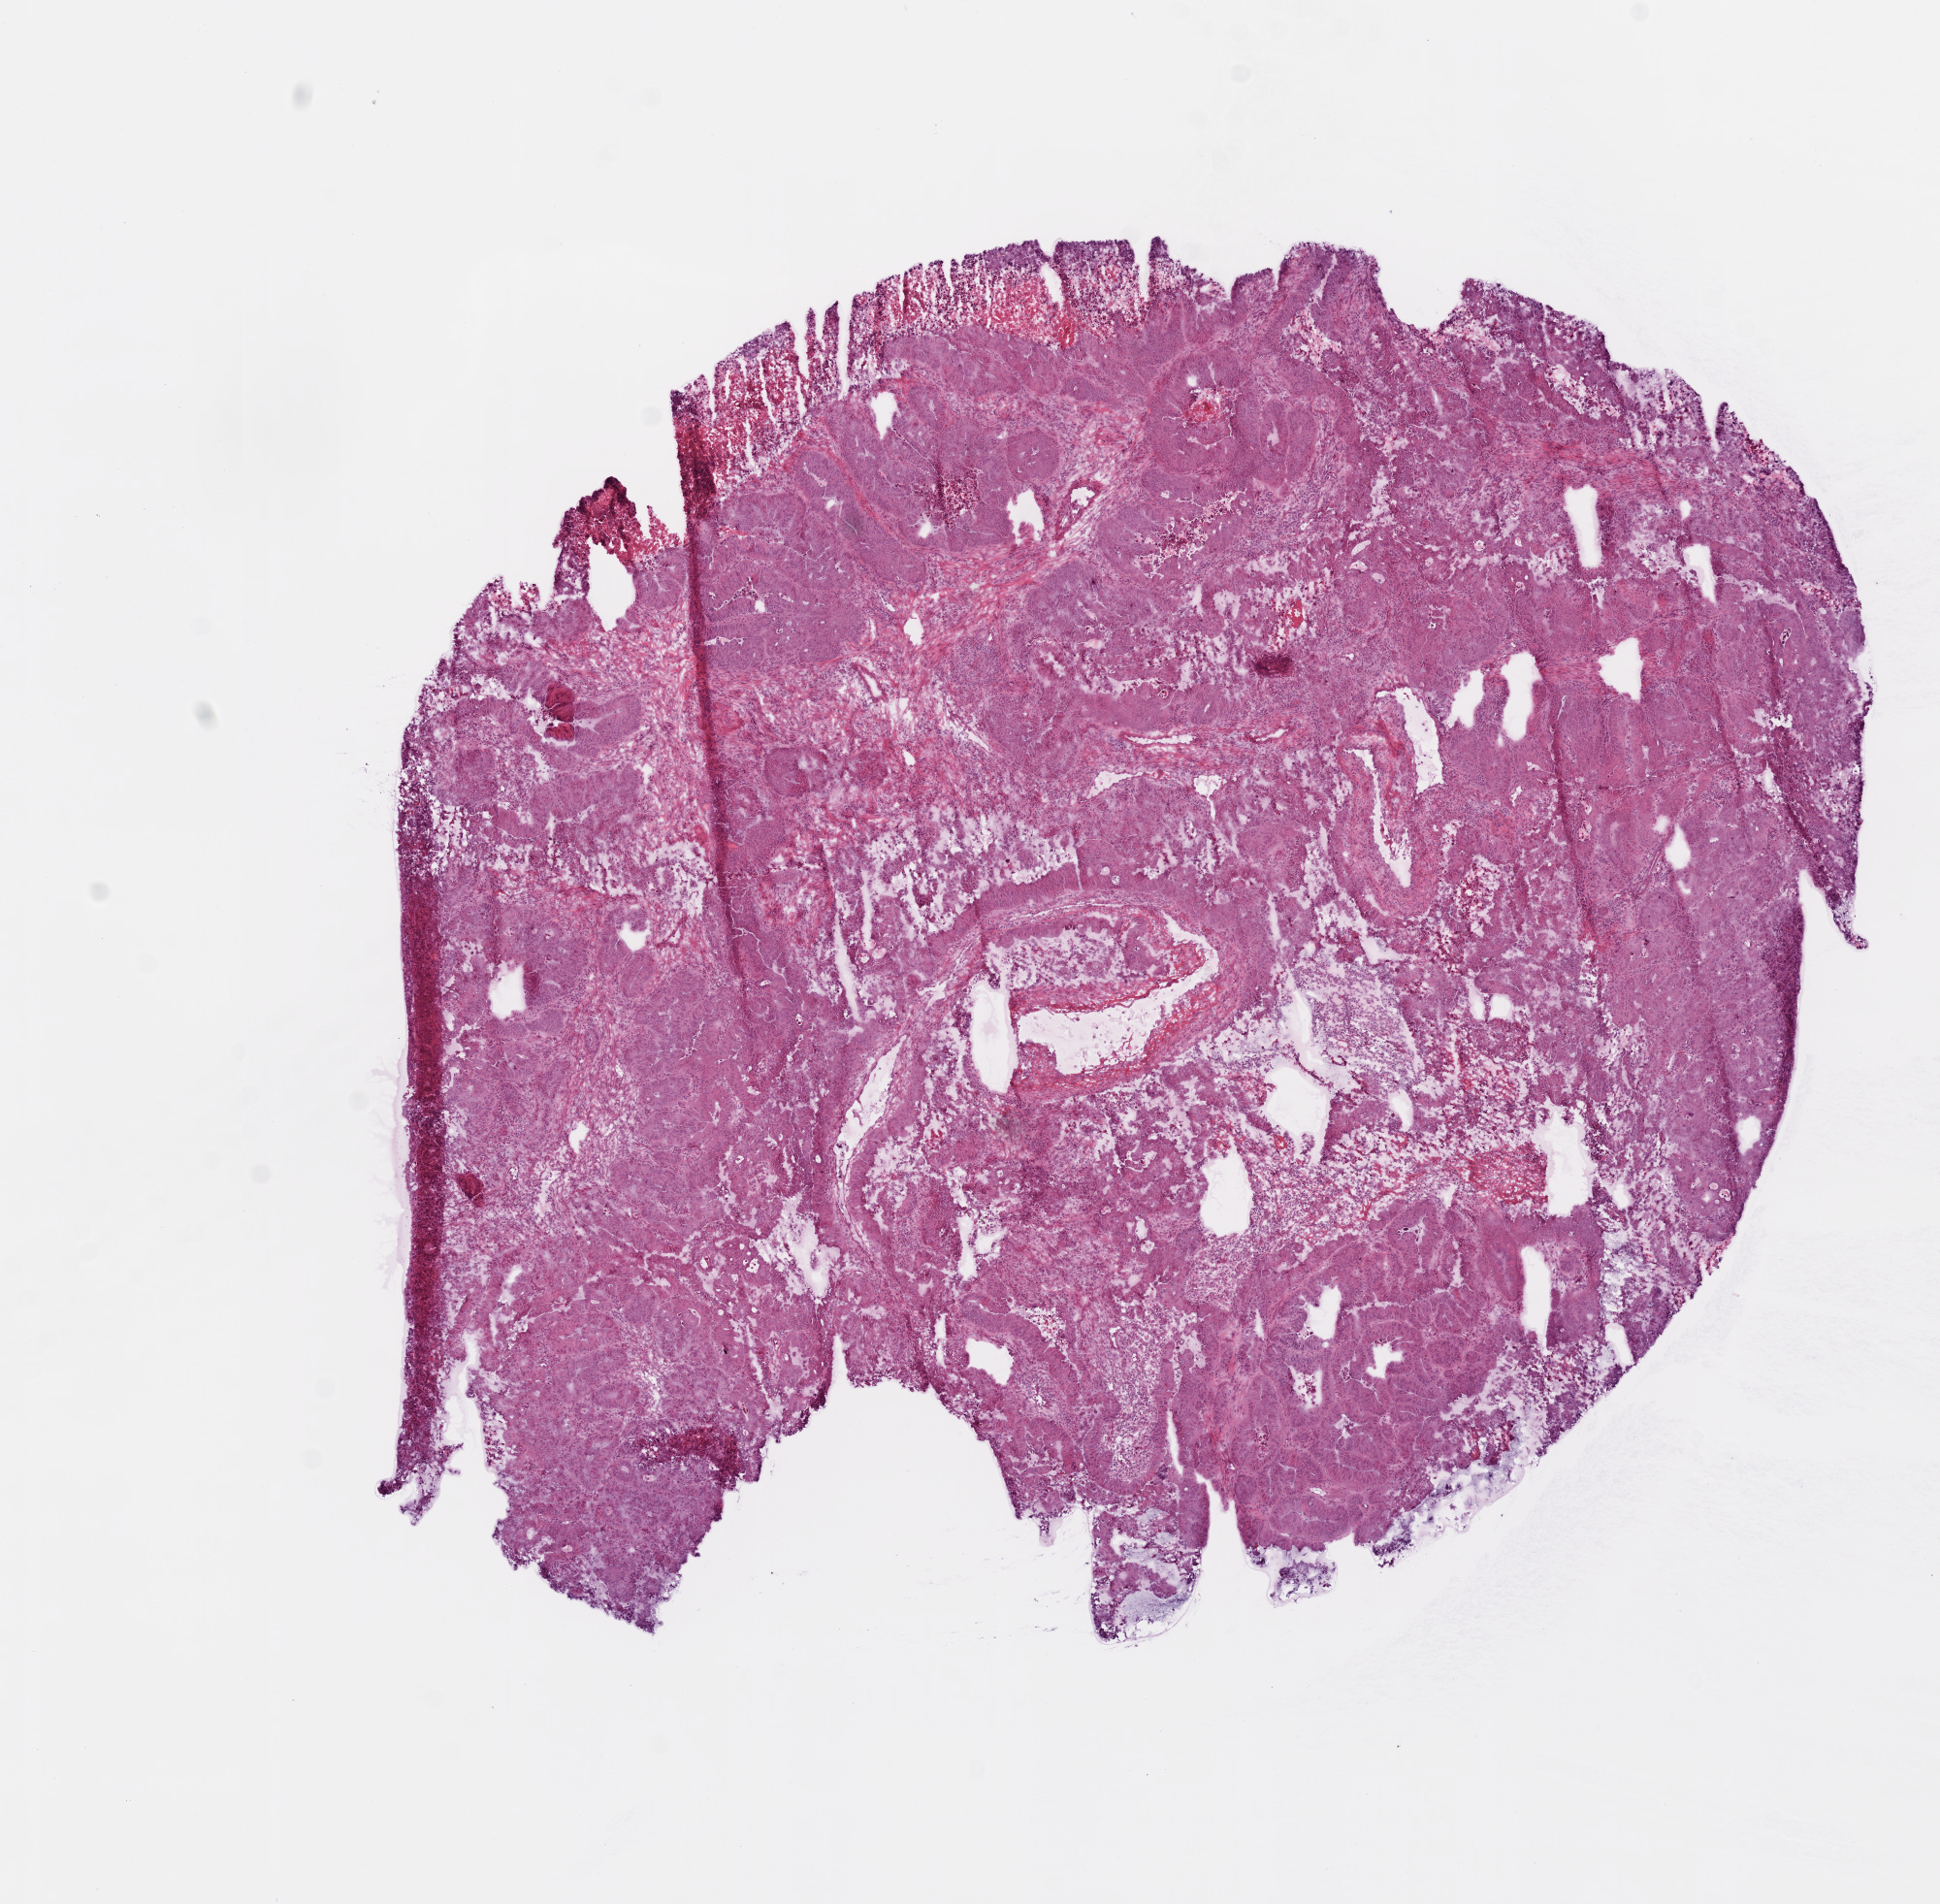
Whole-slide histology image, Hematoxylin and eosin (H&E) stained — whole scanned area (about 8.0 x 7.9 mm) shown as a low-resolution overview. Frozen section. Primary tumour sample from the colon. Male, age 76 years at initial diagnosis. Composition of this section per pathologist review: tumour cells 70%, tumour nuclei 80%, normal cells 0%, stromal cells 10%, necrosis 20%.
AJCC pathologic stage: IV (6th edition). Histologic diagnosis: Adenocarcinoma, NOS (cecum). TNM: T4 N2 M1.